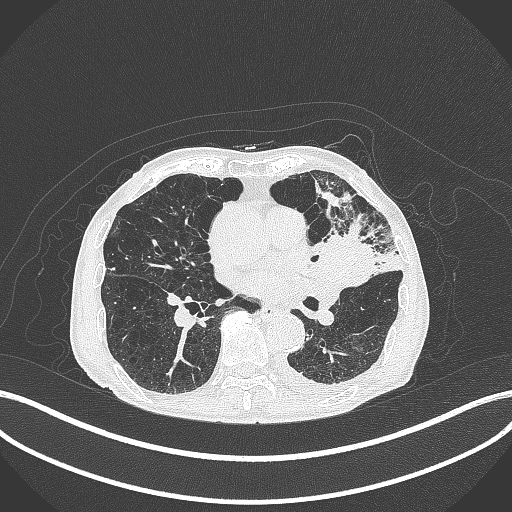
Chest CT, one axial slice. Slice 183 of 385 in the series (ordered by position). Reconstruction kernel B70f. 120 kVp. Lung window (W 1500 / L -600 HU). 1 mm slice thickness. 512 × 512 image matrix. Male patient, age 90 years or older. Case-level facts recorded for this patient, not image findings: clinical TNM (as recorded): T2b N1 M0.
Structures marked on this image (bounding box drawn by a radiologist):
- lung tumour (recorded histology: squamous cell carcinoma): bounding box (x1, y1, x2, y2) in pixels: (315, 231, 373, 296)